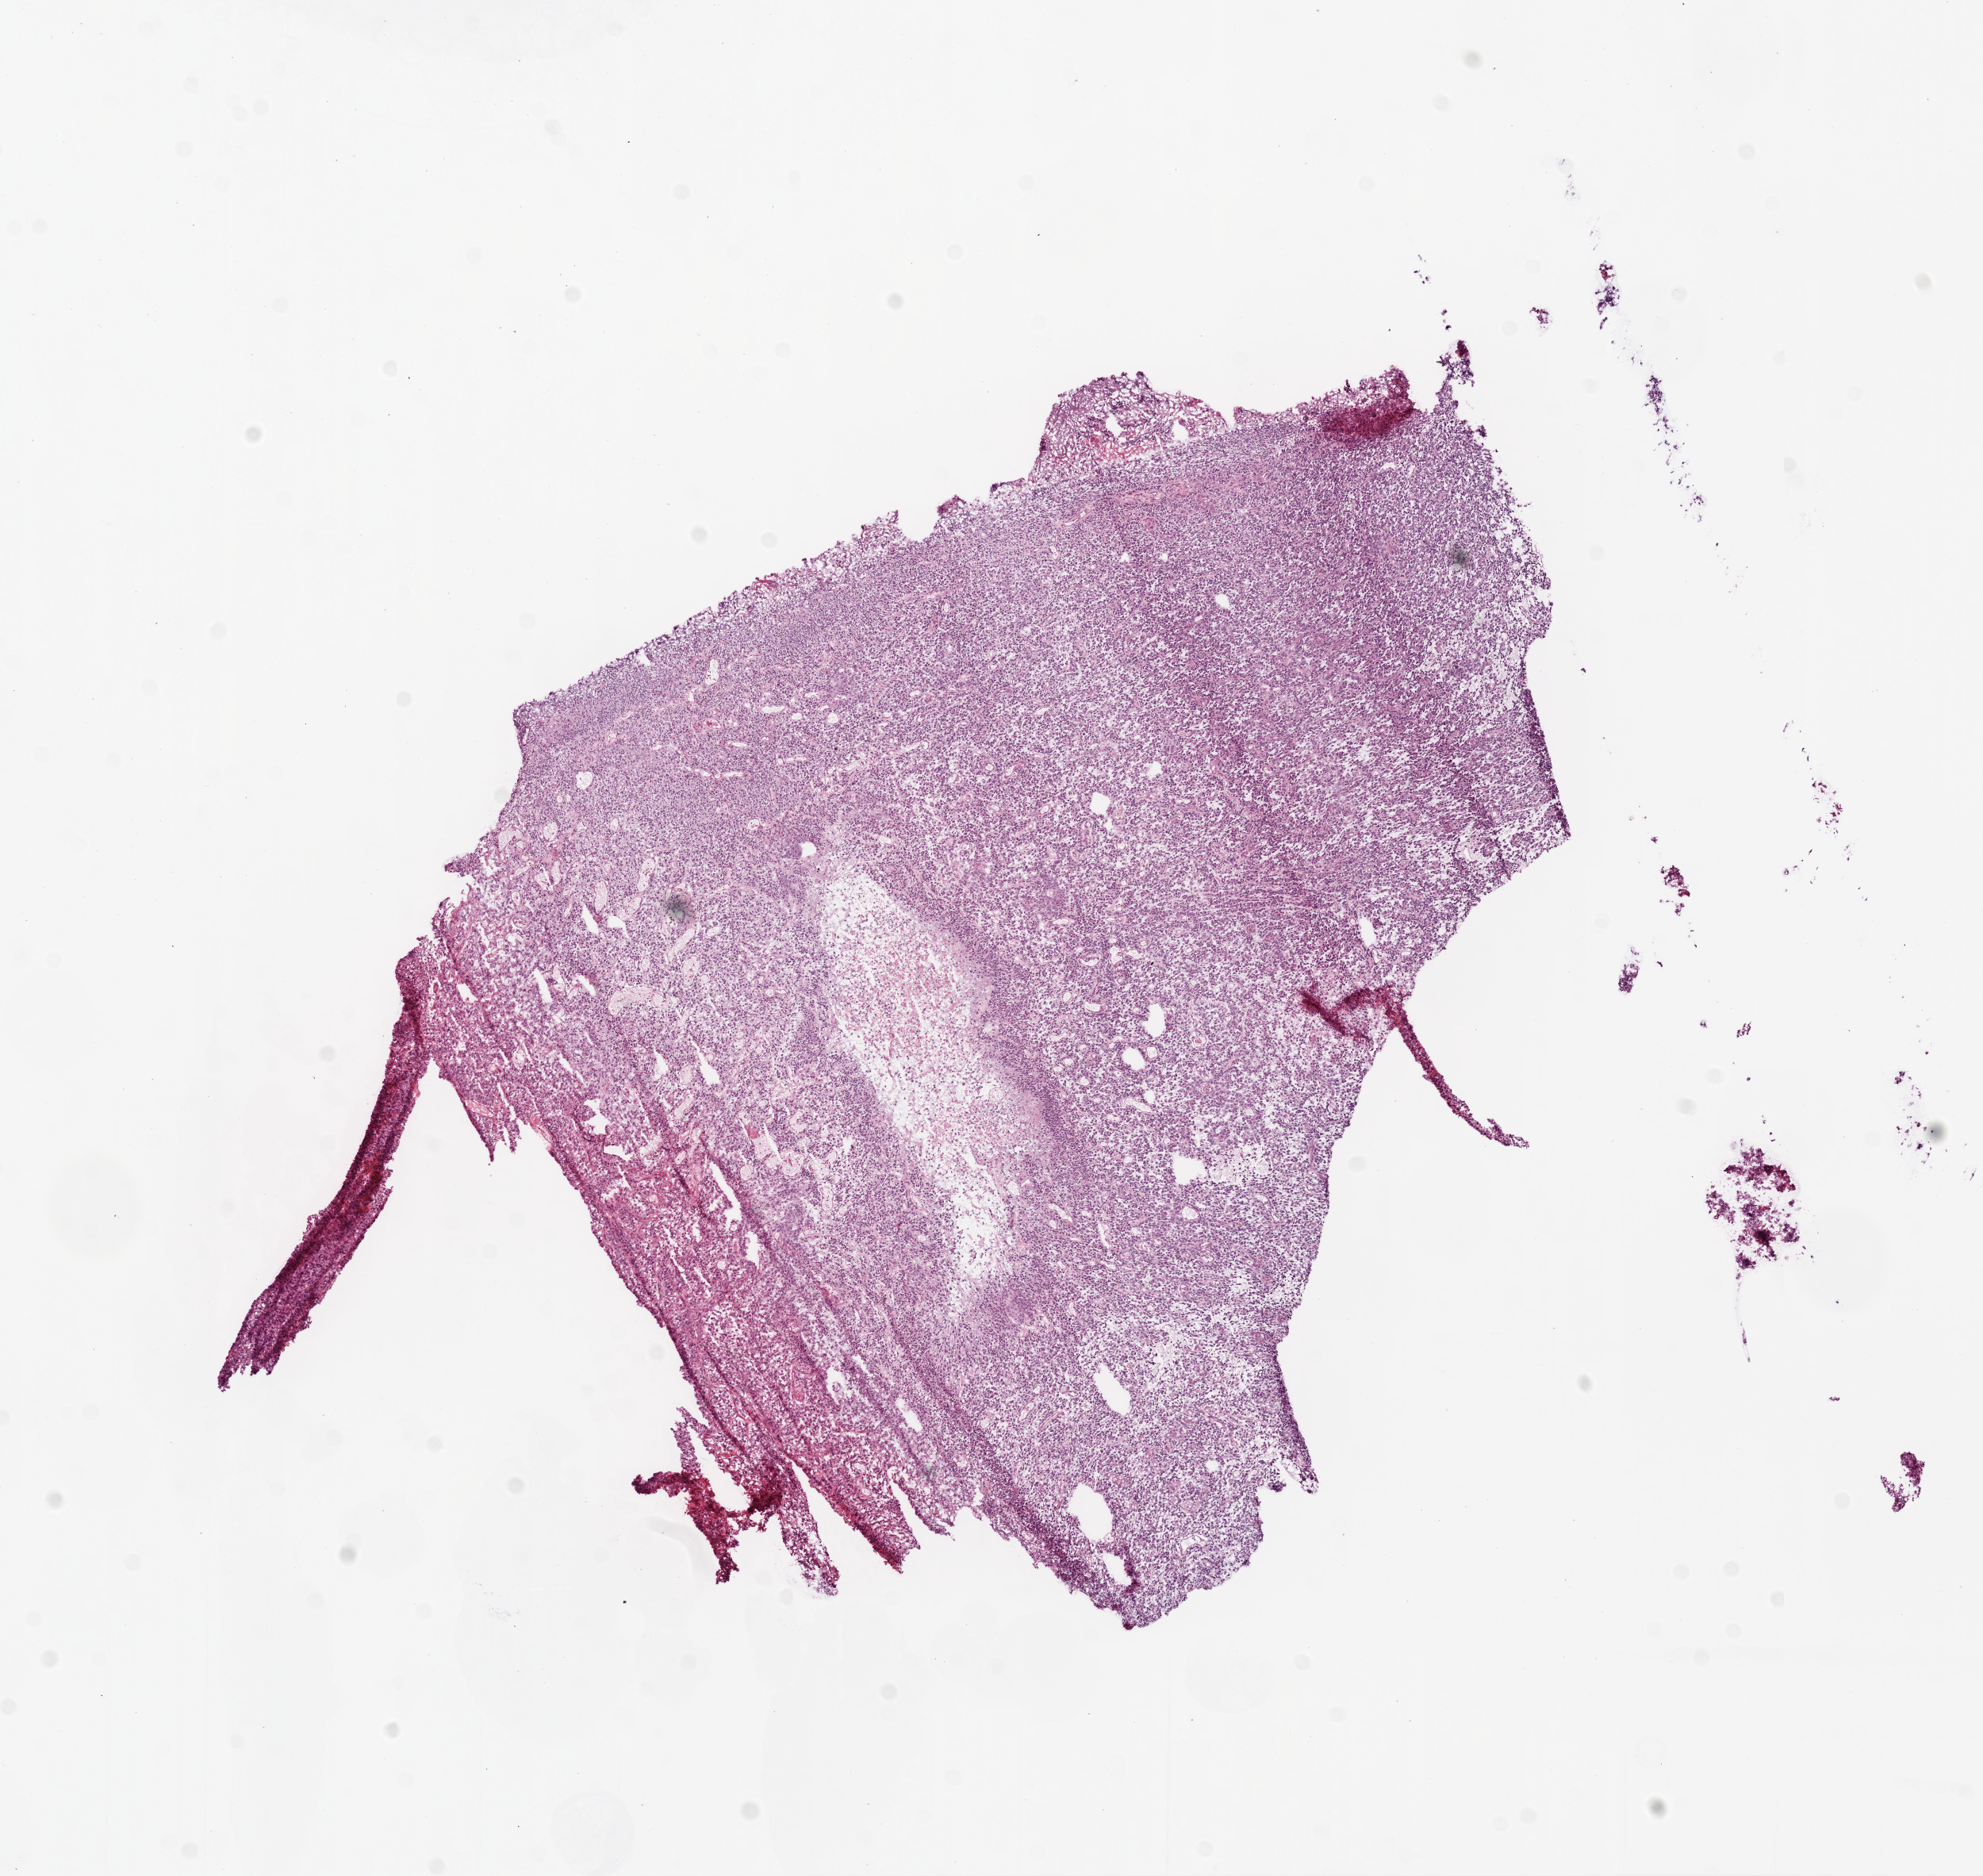
H&E-stained whole-slide image, low-resolution overview of the scanned area, about 10.0 x 9.5 mm. Frozen section. Brain, primary tumour sample. Male, age 57 years at initial diagnosis. Slide review estimates, as recorded: tumour cells 90%, tumour nuclei 95%.
Pathologic diagnosis: Glioblastoma.